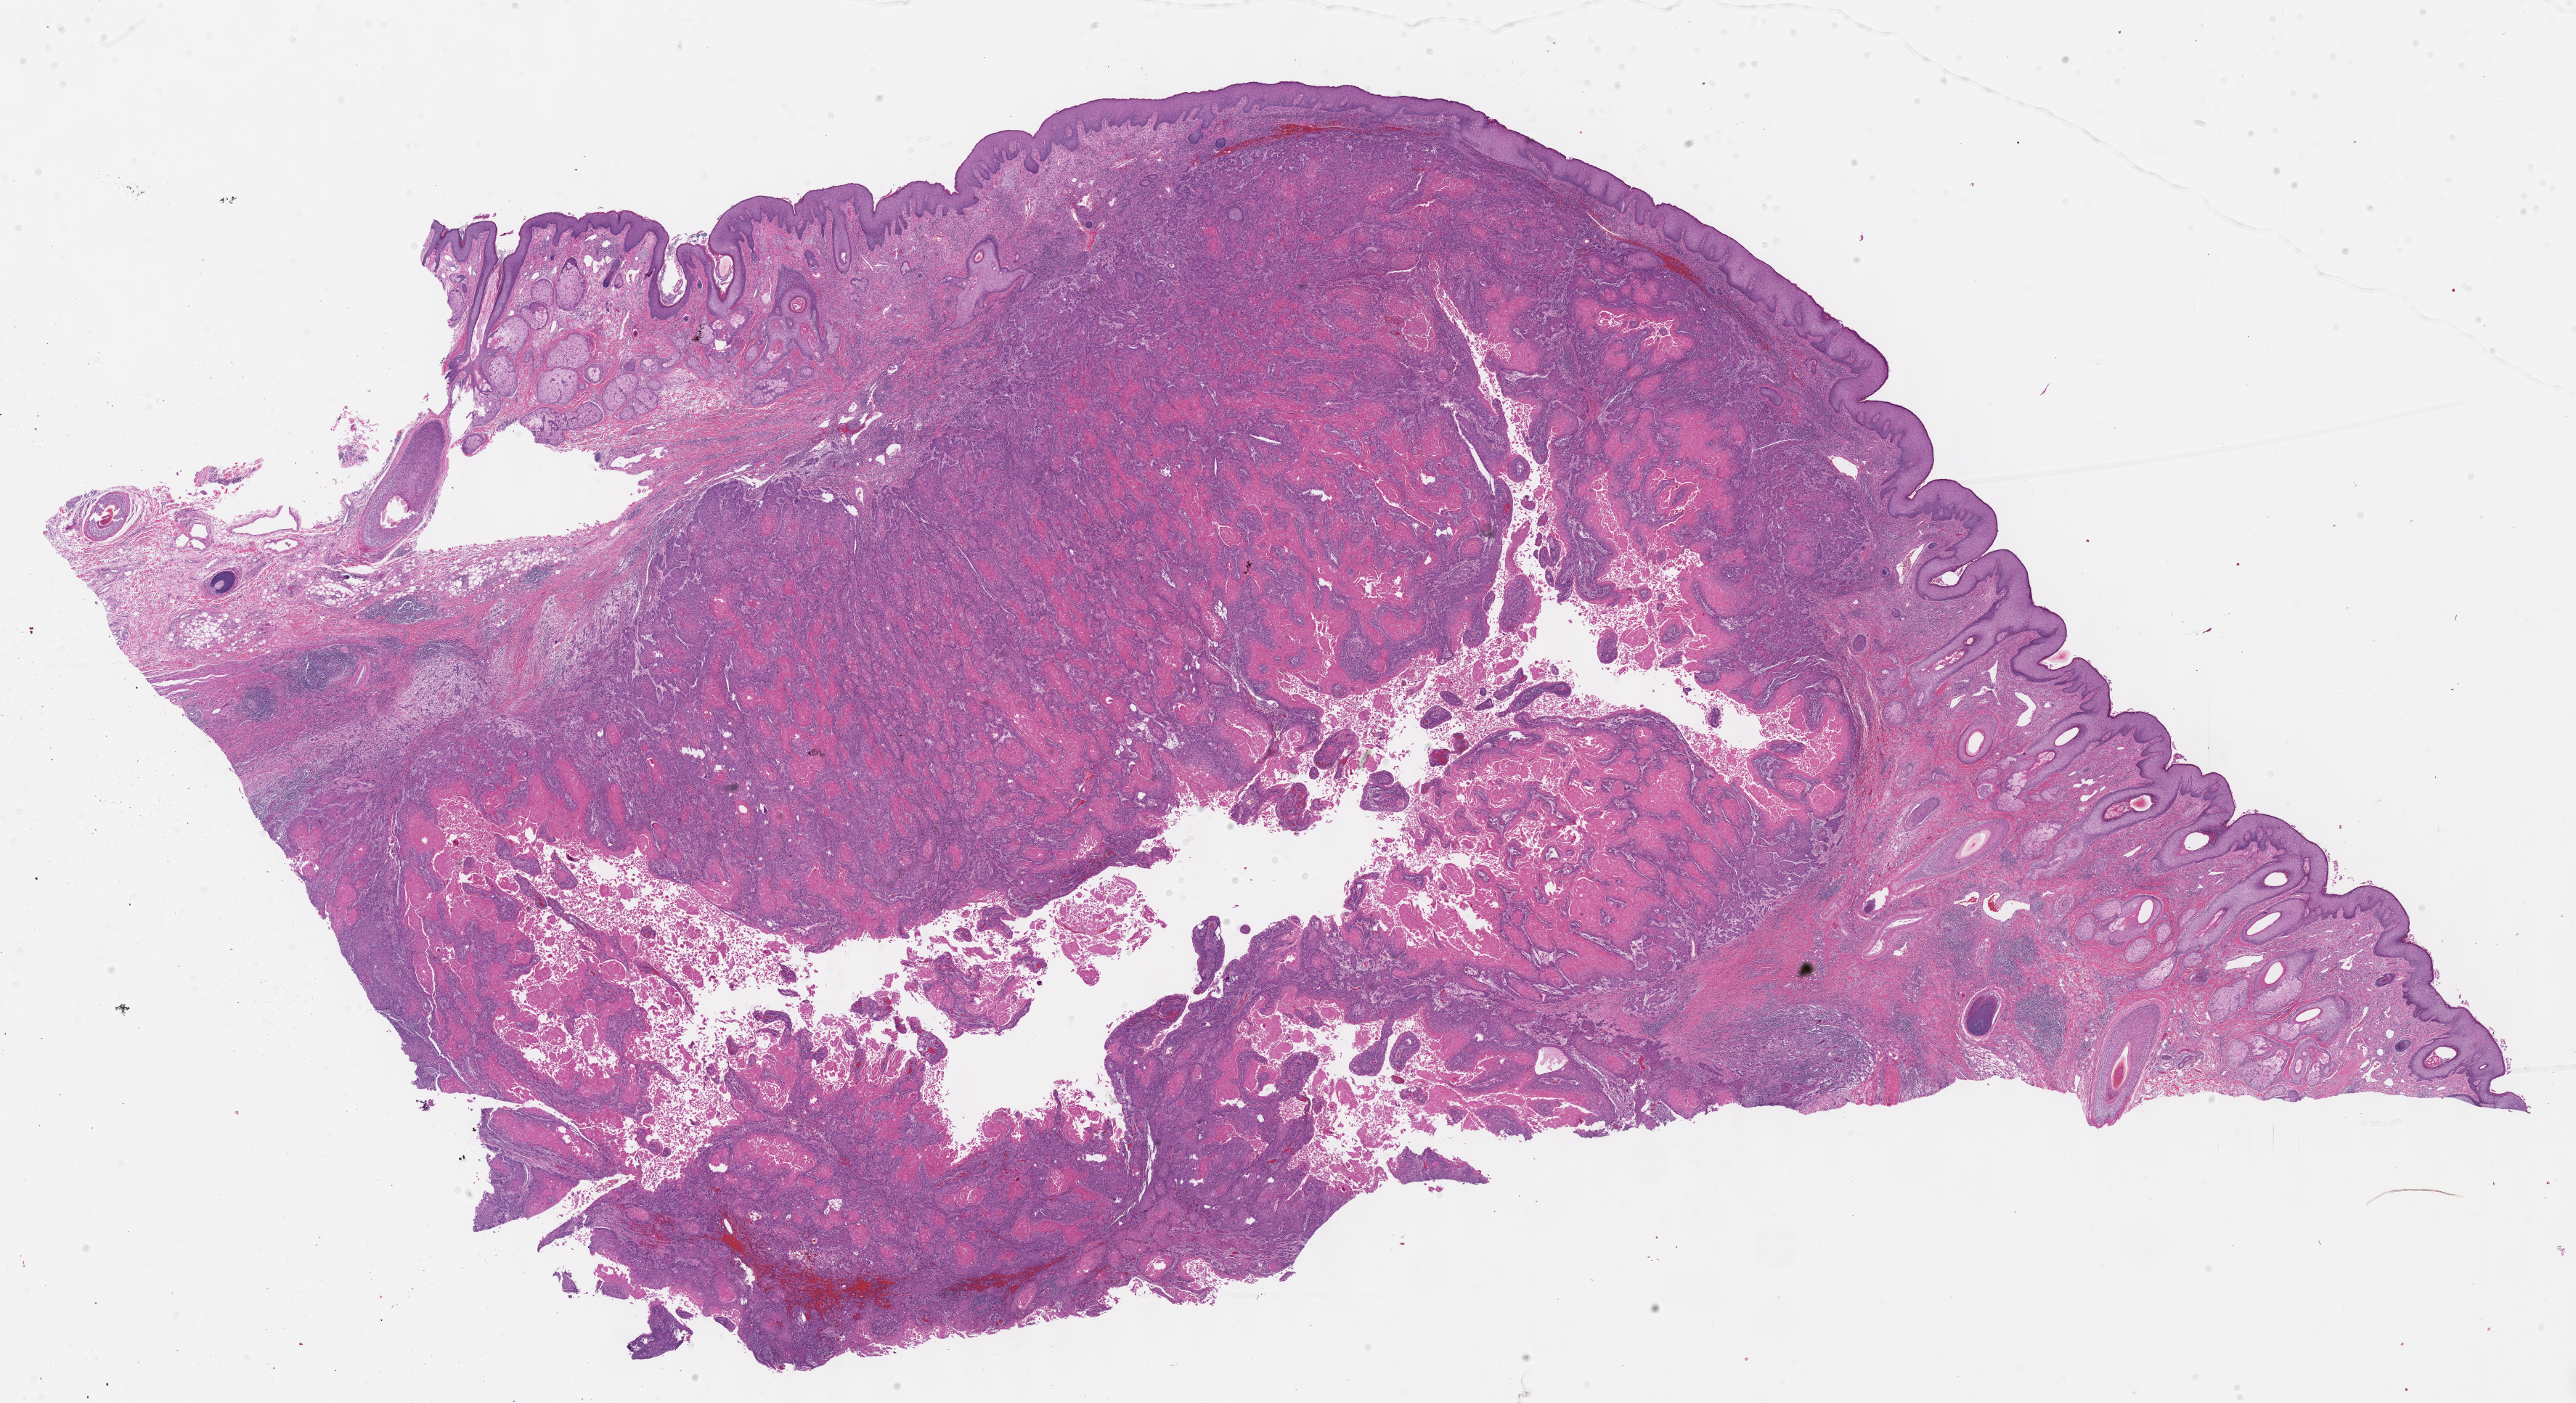
Digitized Hematoxylin and eosin (H&E) stained tissue section (whole slide) — whole scanned area (about 28.7 x 15.6 mm, acquisition: 40x scan) shown as a low-resolution overview, FFPE section, primary tumour sample from the head and neck. Patient: male, age at initial diagnosis 65 years.
Diagnosis: Squamous cell carcinoma, NOS (mouth, NOS).